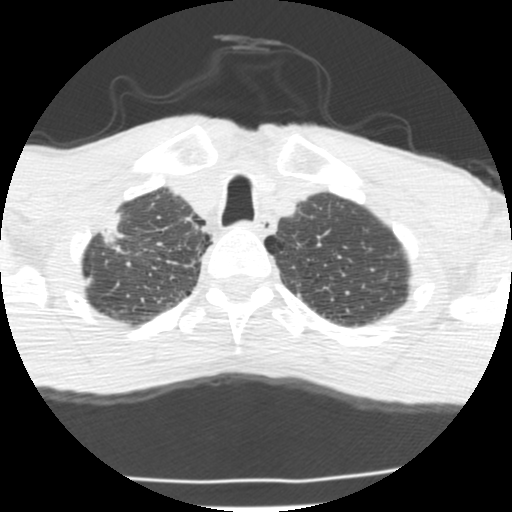
Axial slice from a low-dose chest CT screening exam; second annual screen; lung window (W 1500 / L -600 HU); 2.5 mm slice thickness; standard (soft-tissue) reconstruction kernel (STANDARD); 120 kVp. Male participant, aged 62 years at enrolment.
Expert-annotated lung lesion, bounding box [x1, y1, x2, y2] px = [74, 213, 141, 274]. Screening reader's record for this exam (one nodule recorded; not confirmed to be the boxed lesion): non-calcified nodule or mass ≥4 mm, right upper lobe, 23 × 11 mm, spiculated (stellate) margins, soft tissue attenuation, pre-existing on the prior screen: yes. Official screen result: positive, change unspecified: nodule(s) >= 4 mm or enlarging nodule(s), mass(es), or other non-specific abnormalities suspicious for lung cancer. Participant outcome: lung cancer diagnosed 277 days after this screen — adenocarcinoma, NOS, right upper lobe, poorly differentiated (G3), stage IIA (AJCC 6th edition), 22 mm at pathology.